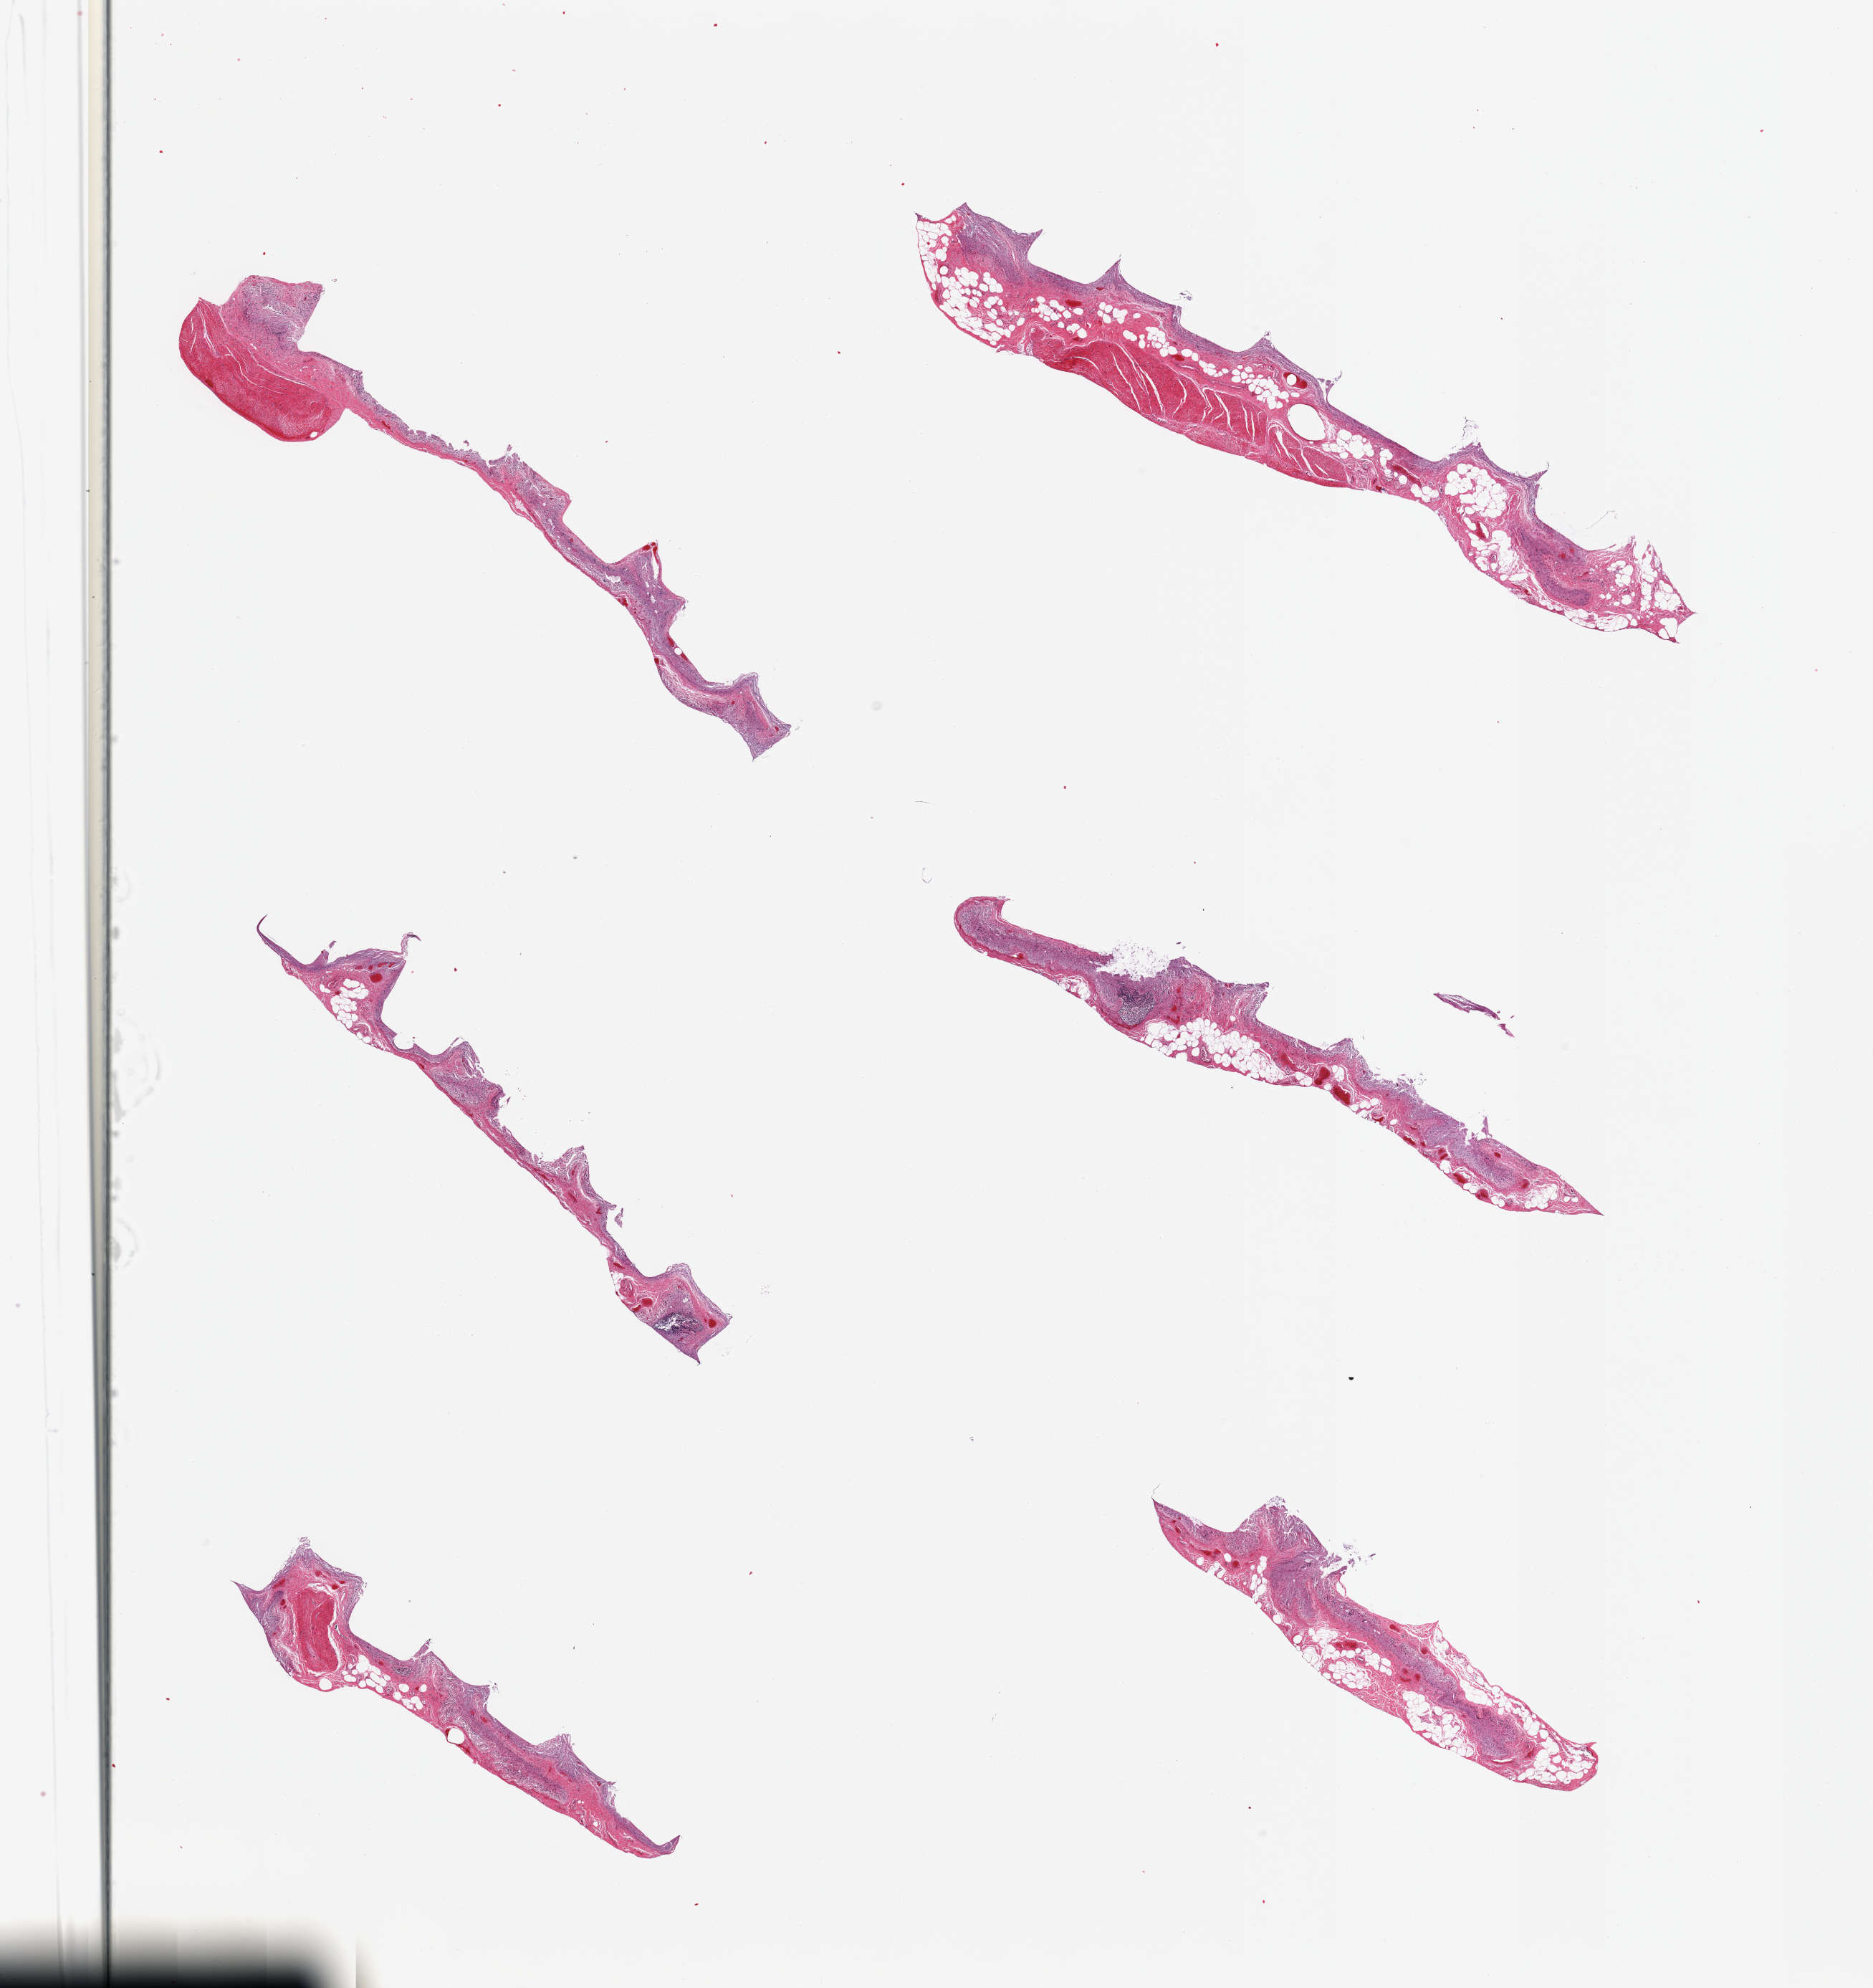
Whole-slide image, H&E stain, brightfield, a low-resolution overview of the entire scanned area, about 20.7 x 21.9 mm (acquisition: 20x scan). PAXgene-fixed paraffin-embedded (PFPE) section. Section of ileum (target tissue). Tissue donor sample. Donor sex: male.
Reviewer comment on this tissue sample: 6 pieces; autolyzed mucosa and <5% residual lymphoid aggregates.